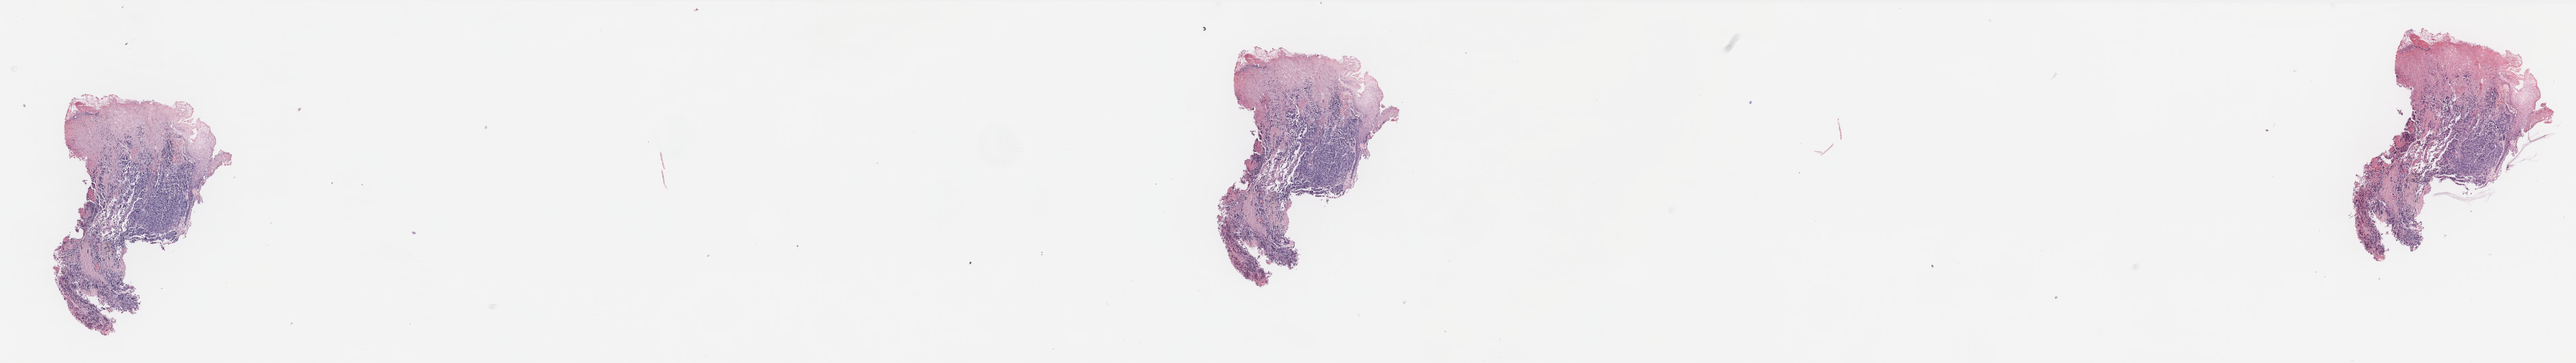
H&E-stained whole-slide image, low-resolution overview of the scanned area, about 30.3 x 4.3 mm (from a 40x scan); formalin-fixed paraffin-embedded (FFPE) diagnostic section; skin, primary tumour sample. Female, age 63 years at initial diagnosis.
• diagnosis: Malignant melanoma, NOS